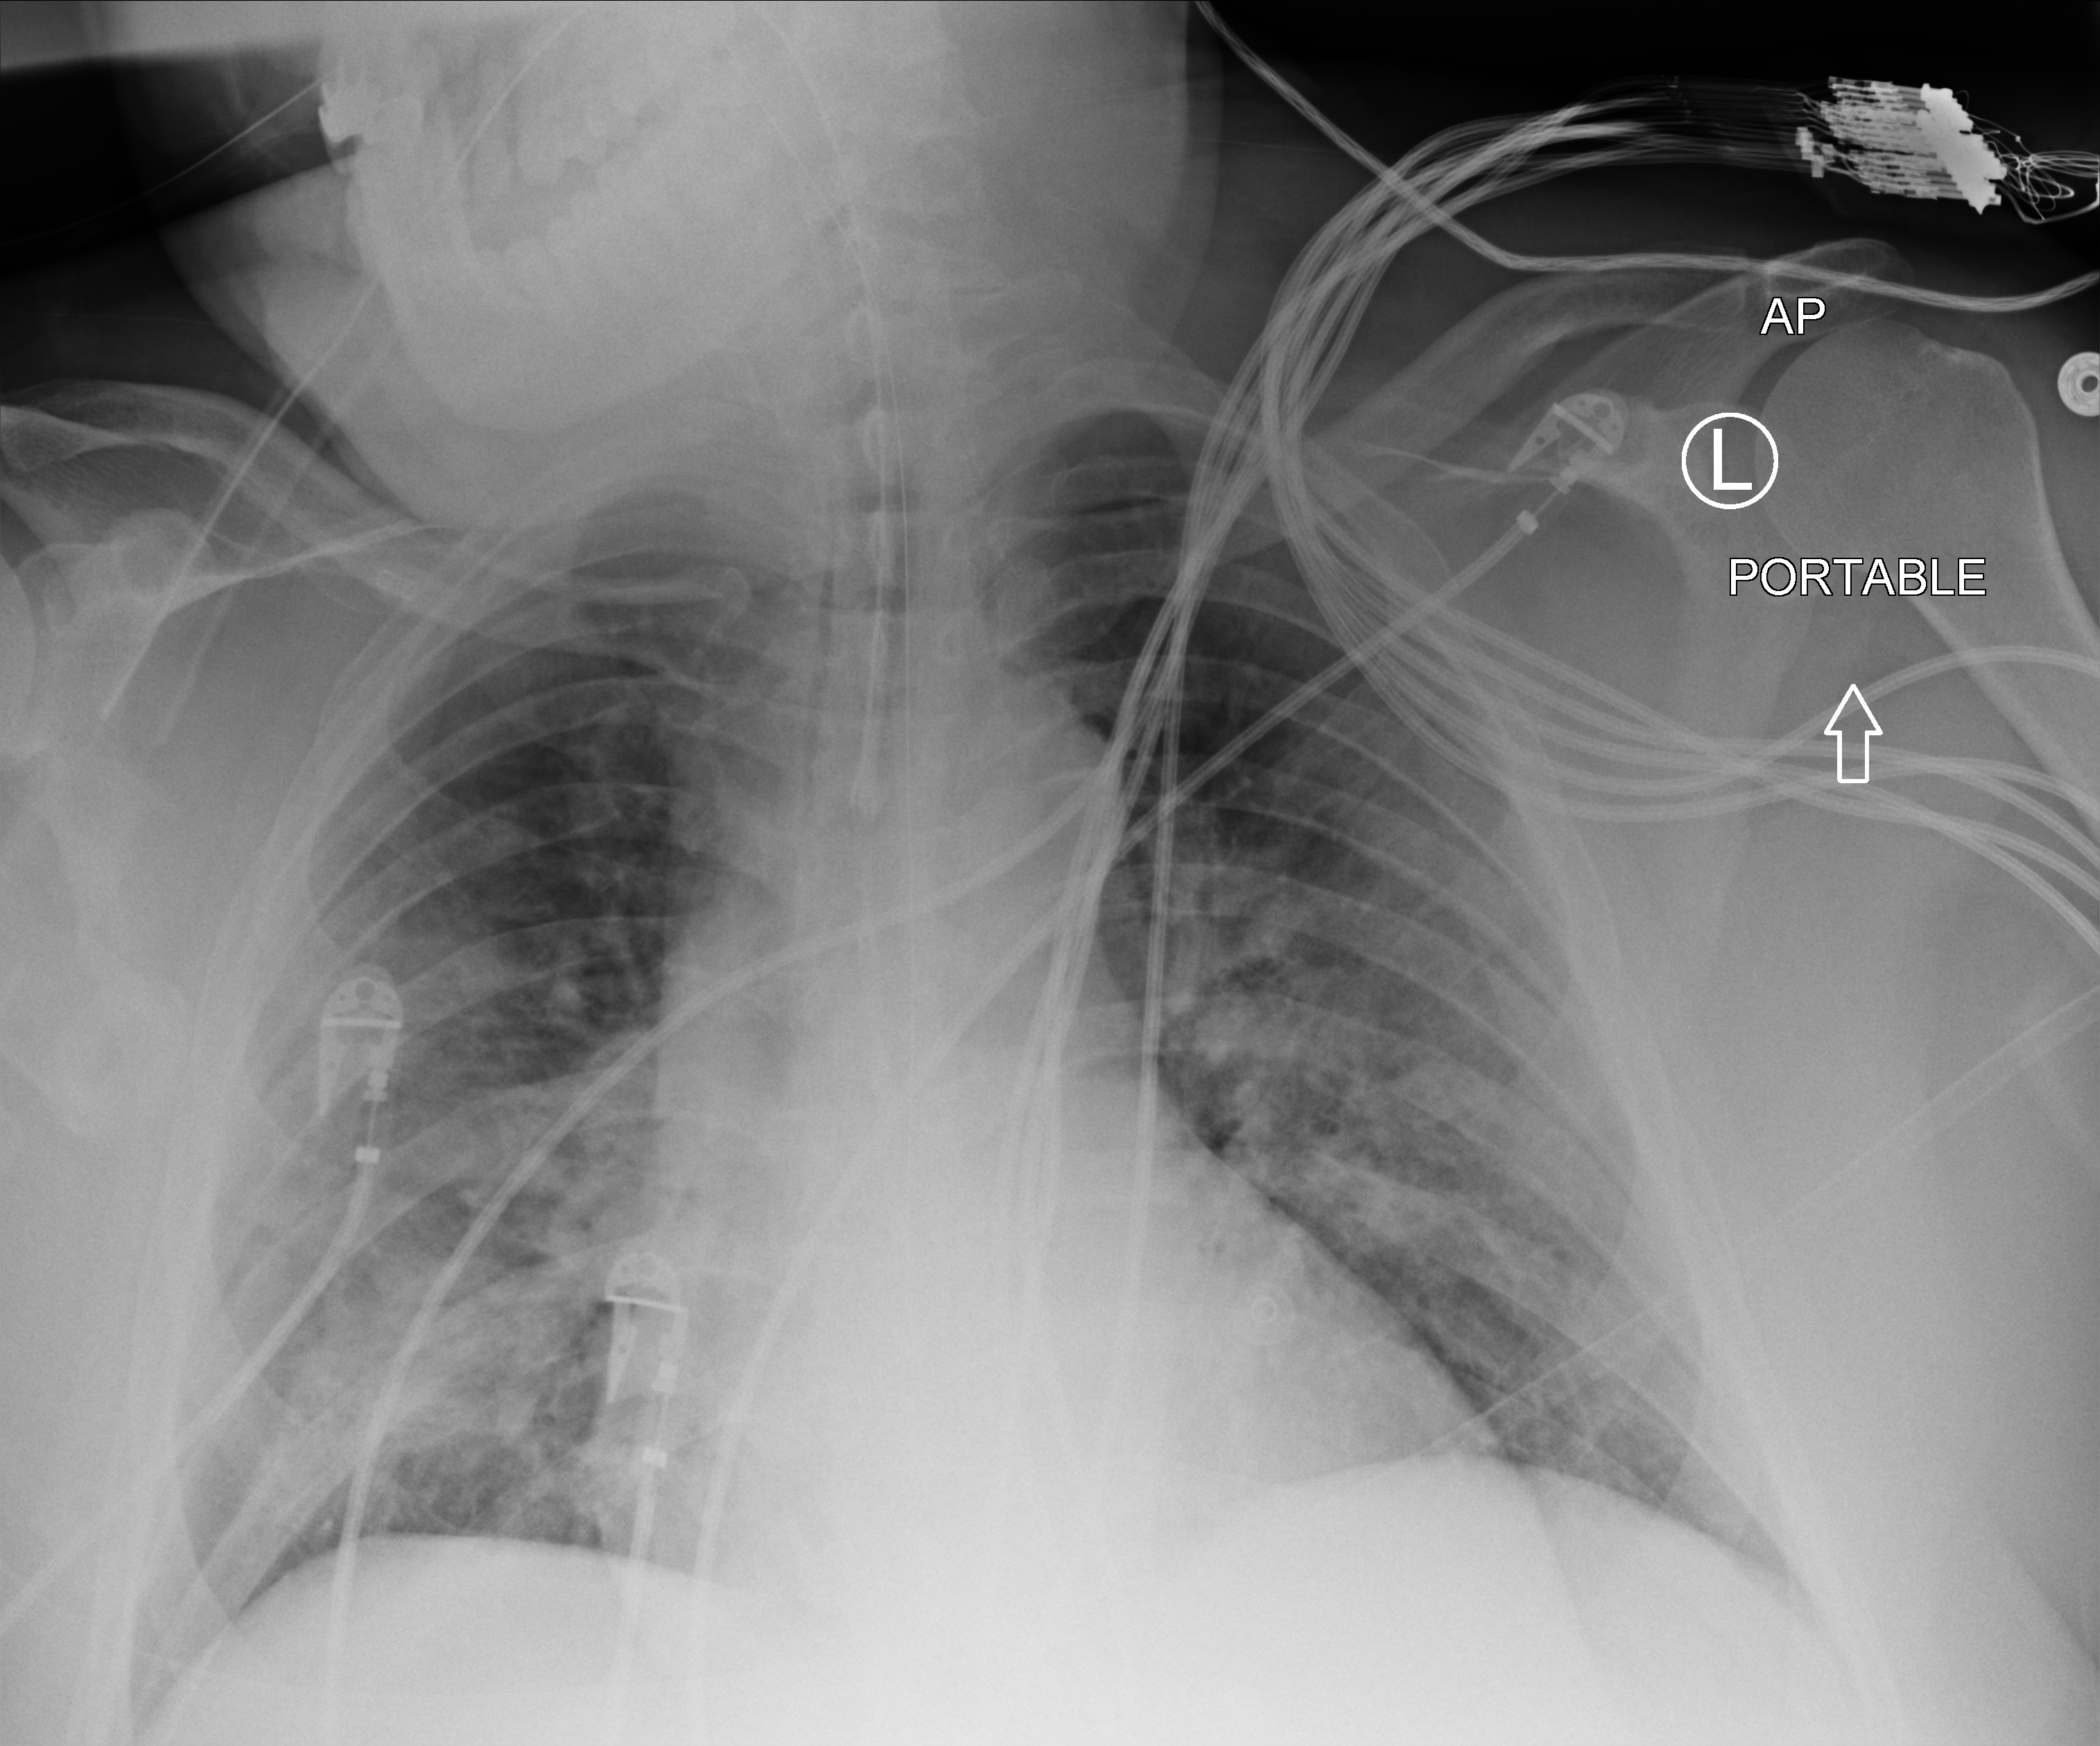
Portable chest radiograph. Male patient hospitalised with COVID-19, age 60–74 years.
From the hospital-stay record, not from the radiograph (when in the stay this image was taken is not recorded): admitted to intensive care during this hospital stay: yes; length of hospital stay: 17 days; mechanically ventilated during this hospital stay: yes.